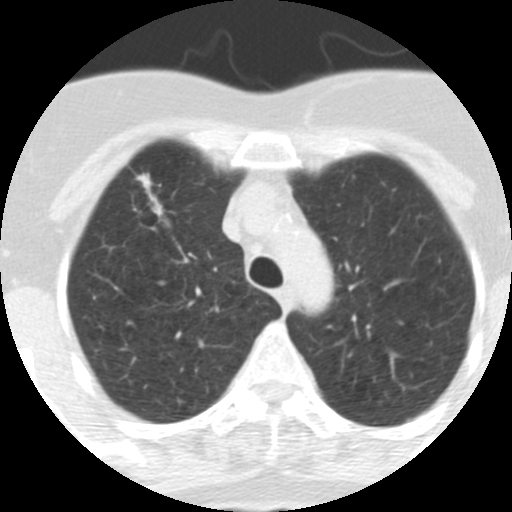
Low-dose screening chest CT, axial slice; baseline annual screen; lung window (W 1500 / L -600 HU); 2.5 mm slice thickness; 120 kVp; slice 67 of 313 in the series; 512 × 512 image matrix. Female, age 62 years at enrolment.
Lesion marked by an expert reader, bounding box (x1, y1, x2, y2) in pixels: (116, 166, 186, 235). Reader record for this screening exam (exam-level; its link to the box is not recorded): non-calcified nodule or mass ≥4 mm, right upper lobe, 9 × 7 mm, spiculated (stellate) margins, soft tissue attenuation.